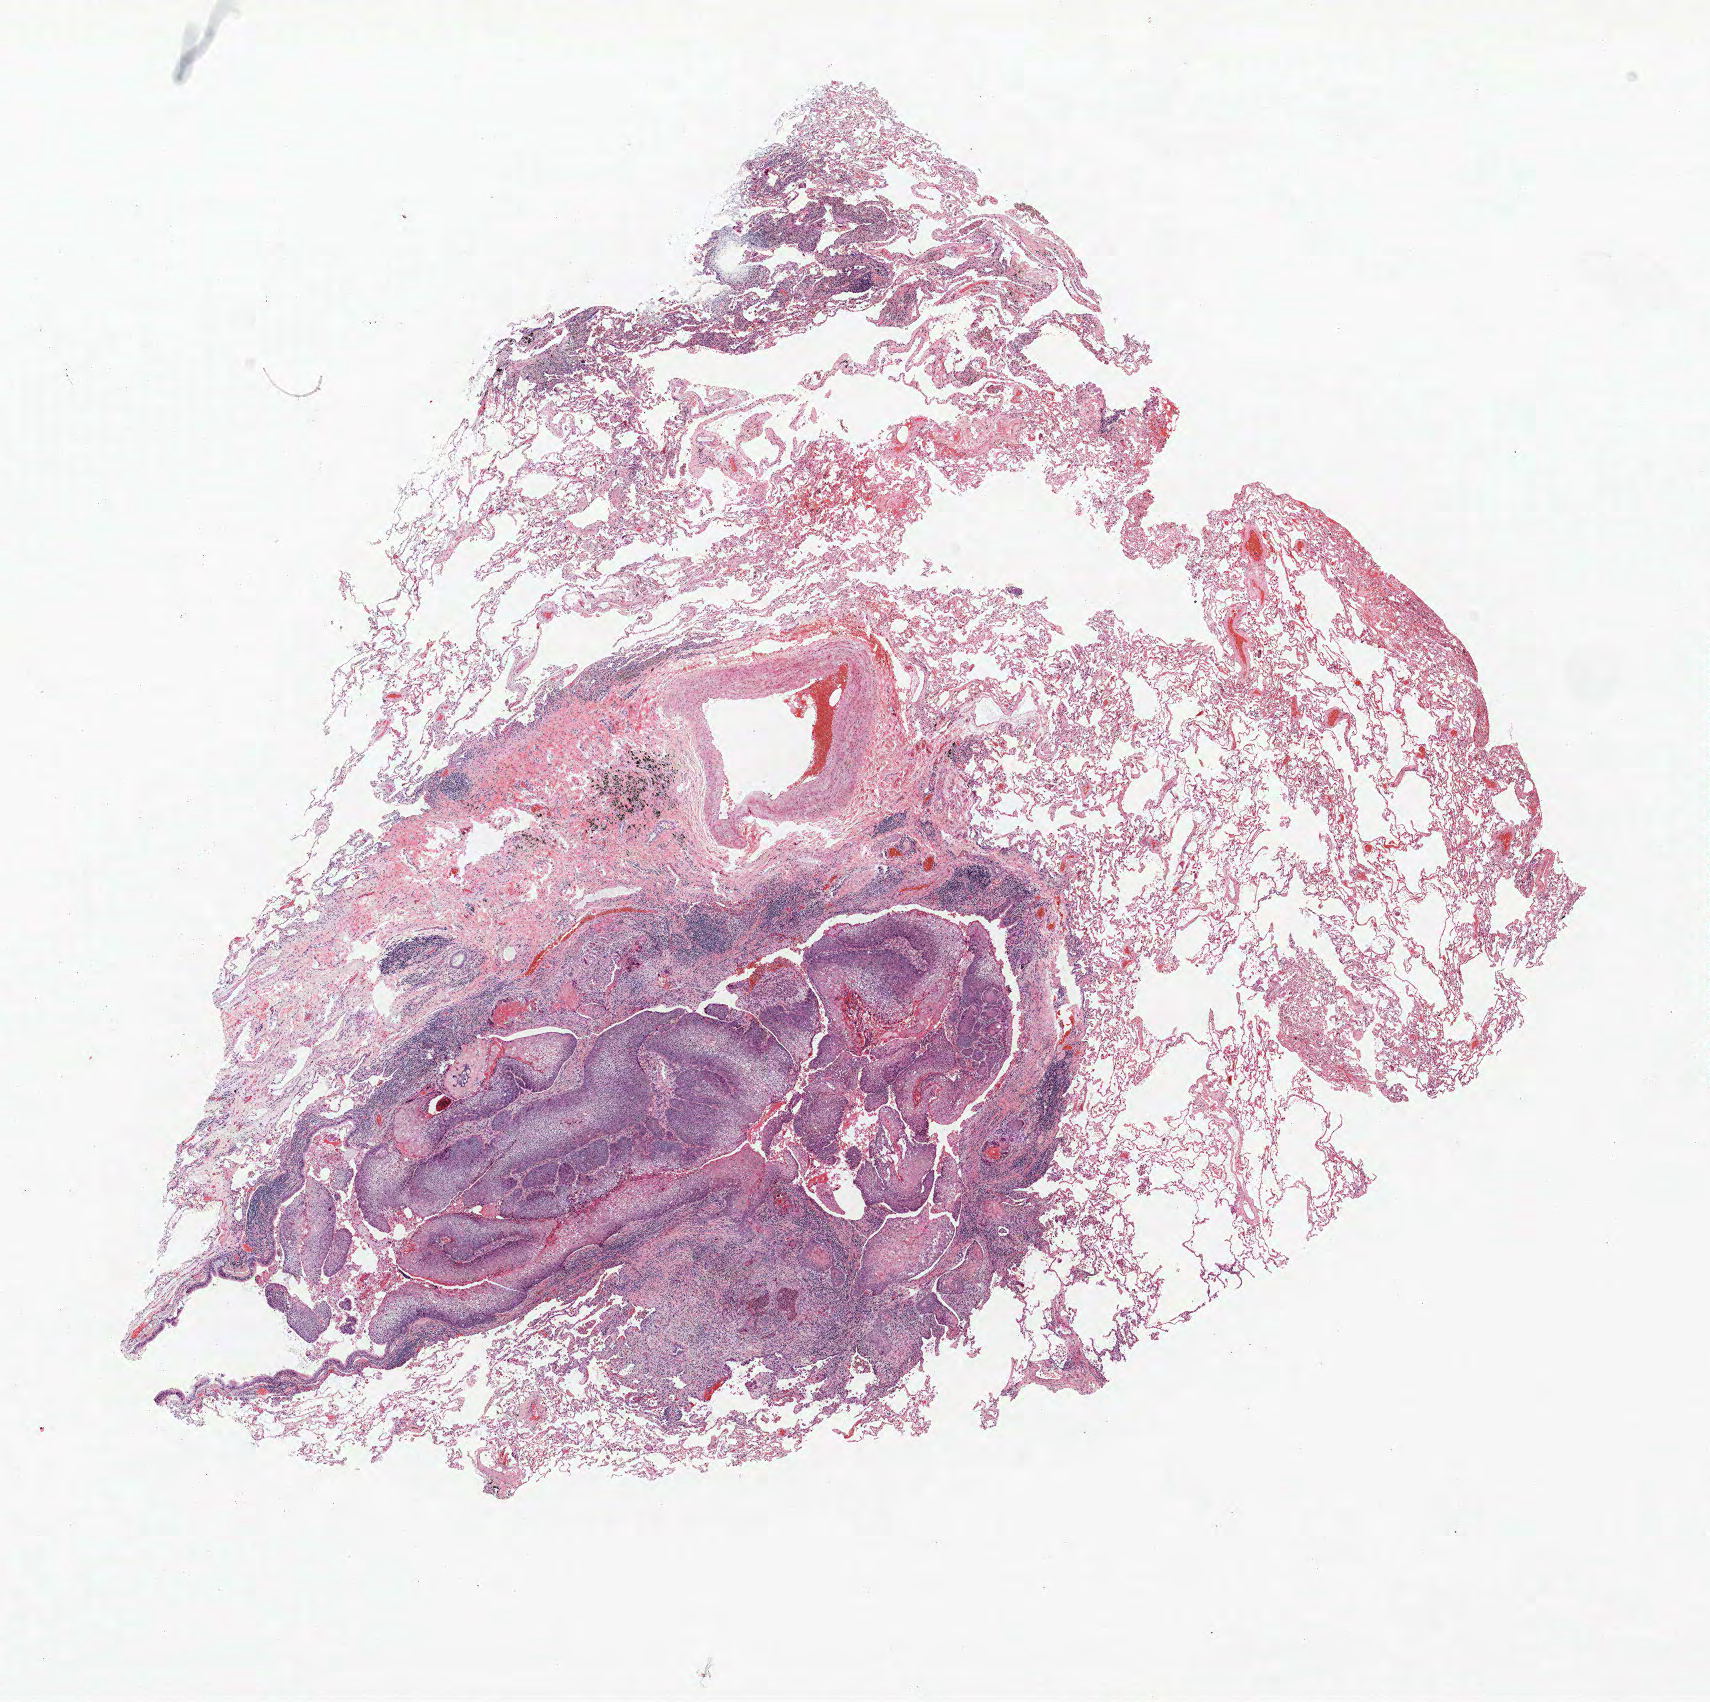
Hematoxylin and eosin (H&E) stained whole-slide image, shown as a low-resolution overview of the whole scanned area (about 13.7 x 13.6 mm, from a 40x scan), formalin-fixed paraffin-embedded (FFPE) section, lung tissue. Male patient, aged 58 at enrolment. Current smoker at enrolment.
Participant's lung-cancer diagnosis: Bronchiolo-alveolar adenocarcinoma, NOS. Note: participant had 2 primary lung cancers recorded; fields above describe the first.